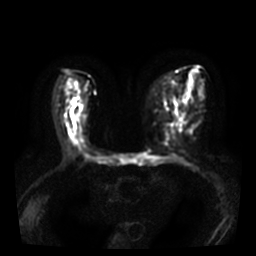
Breast MRI, one axial slice. Position 15 of 36 along the scan axis. Diffusion-weighted series; image 2 of 4 stored at this slice position (different b-values; order by instance number). 3 T. 5 mm slice thickness. 256 × 256 image matrix, field of view 320 × 320 mm. Female patient.
Outlined on this slice (outlined manually by an expert reader):
- tumour on diffusion-weighted imaging: bounding box <72,103,75,106> (left, top, right, bottom; pixels)